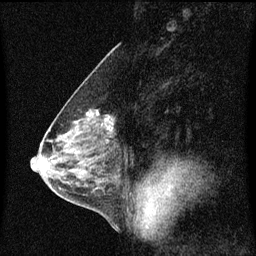
Breast MRI (dynamic contrast-enhanced), one sagittal slice; slice 35 of 60 in the series (ordered by position); dynamic contrast-enhanced series, image 2 of 3 at this slice position (ordered by acquisition); 1.5 T; TE 4.2 ms, TR 8.4 ms; 2 mm slice thickness; 256 × 256 image matrix. Female patient, age 58 years.
Outlined on this slice (semi-automatic segmentation, software-assisted and operator-edited):
- analysis volume of interest (the breast-tissue region the enhancement analysis was run in; not a lesion): bounding box [x1, y1, x2, y2] px = [79, 108, 117, 143]
- tumour enhancement mask (voxels above the 70 % enhancement threshold inside the analysis volume of interest): [87, 112, 114, 131]